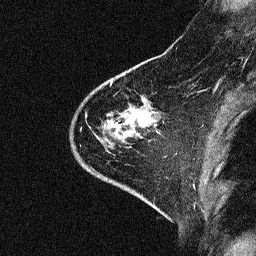
Breast MRI (dynamic contrast-enhanced), one sagittal slice; slice 16 of 64 in the series (ordered by position); dynamic contrast-enhanced study with each time point stored as its own series, time point 2 of 3 at this slice position (early post-contrast, ordered by acquisition time); 1.5 T; TE 4.5 ms, TR 11 ms; 256 × 256 image matrix. Patient: female, 46 years. From the clinical record (not read from this slice): setting: breast cancer imaged before/during neoadjuvant chemotherapy; receptor status: HER2-positive.
Annotated regions visible in this slice (semi-automatically segmented with operator editing):
- analysis volume of interest (the breast-tissue region the enhancement analysis was run in; not a lesion): box from (x=46, y=51) to (x=180, y=169) px
- tumour enhancement mask (voxels above the 90 % enhancement threshold inside the analysis volume of interest): (x=104, y=121)–(x=117, y=130)